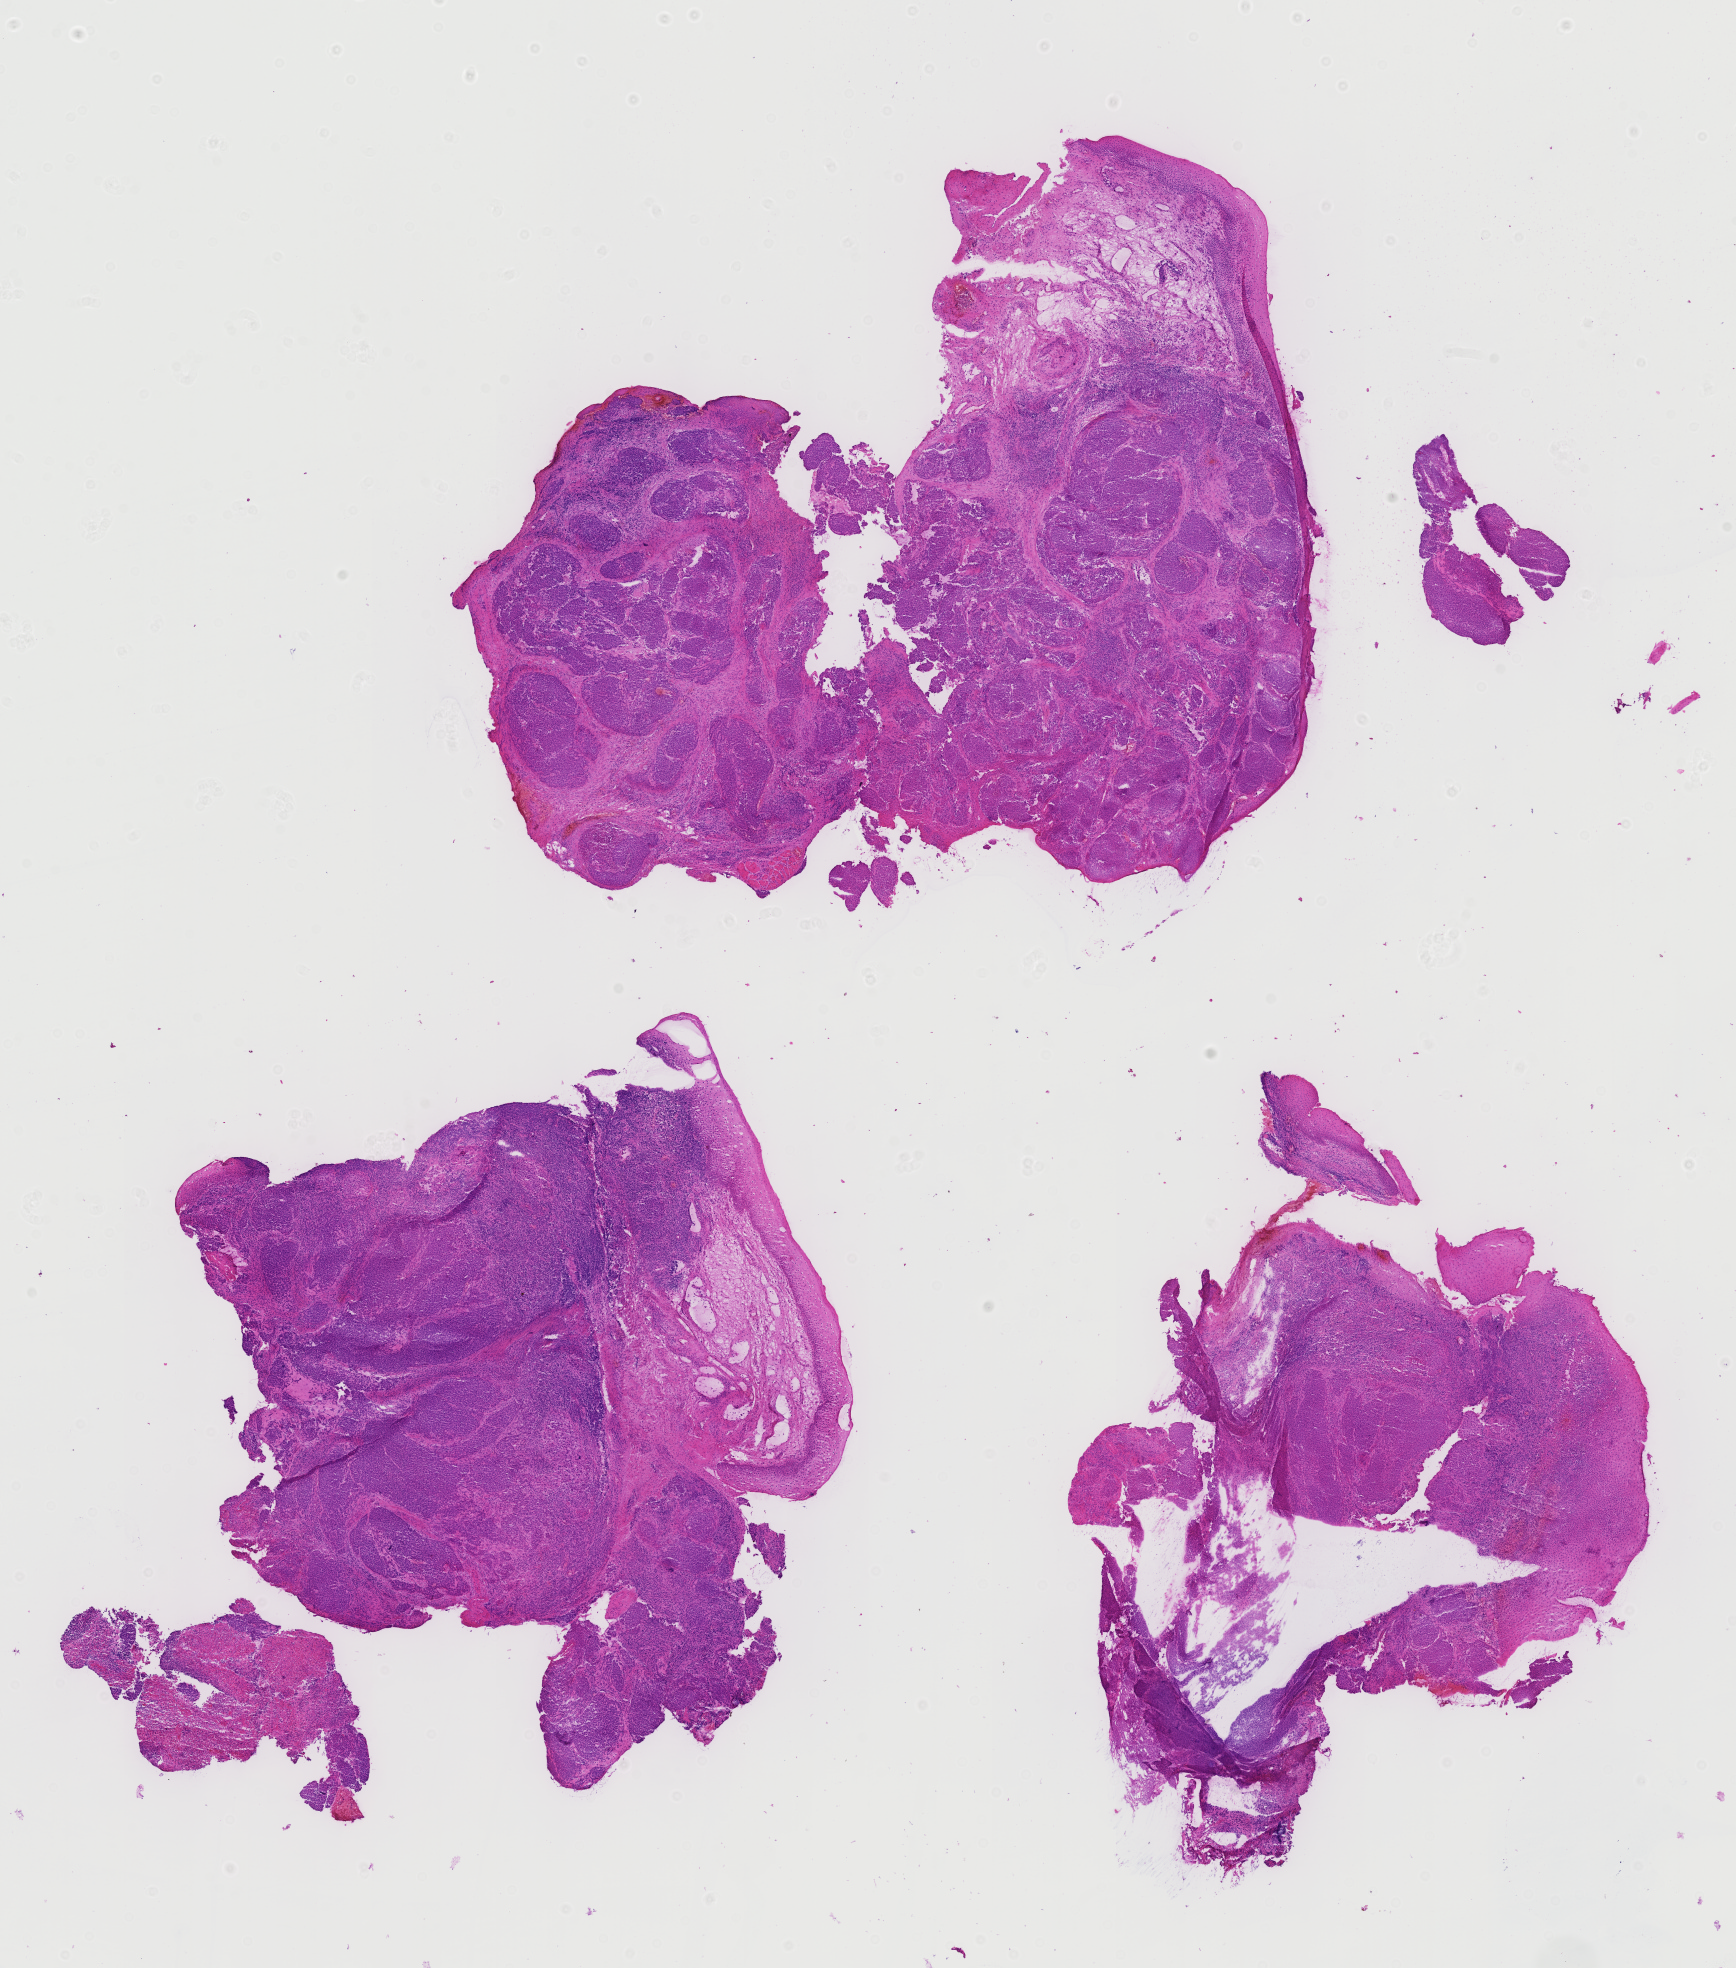
Whole-slide histology image, Hematoxylin and eosin (H&E) stained, shown as a low-resolution overview of the whole scanned area (about 12.6 x 14.3 mm). Formalin-fixed paraffin-embedded (FFPE) diagnostic section. Sample: primary tumour, head and neck. Male, age 61 years at initial diagnosis. Histologic grade: GX (grade cannot be assessed).
• histologic diagnosis: Squamous cell carcinoma, large cell, nonkeratinizing, NOS (tonsil, NOS)